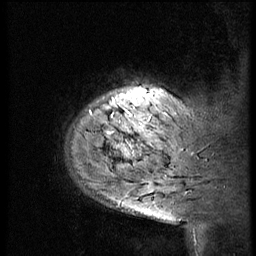
Breast MRI (dynamic contrast-enhanced), one sagittal slice; slice 8 of 56 in the series (ordered by position); 3 images stored at this slice position (order not interpretable as contrast timing); 1.5 T; TE 4.2 ms, TR 9 ms; 256 × 256 image matrix. Patient: female, 51 years. From the clinical record (not read from this slice): setting: breast cancer imaged before/during neoadjuvant chemotherapy; receptor status: triple-negative.
Annotated regions visible in this slice (semi-automatically segmented with operator editing):
- analysis volume of interest (the breast-tissue region the enhancement analysis was run in; not a lesion): bounding box (x1, y1, x2, y2) in pixels: (63, 70, 183, 179)
- tumour enhancement mask (voxels above the 140 % enhancement threshold inside the analysis volume of interest): (117, 92, 146, 157)